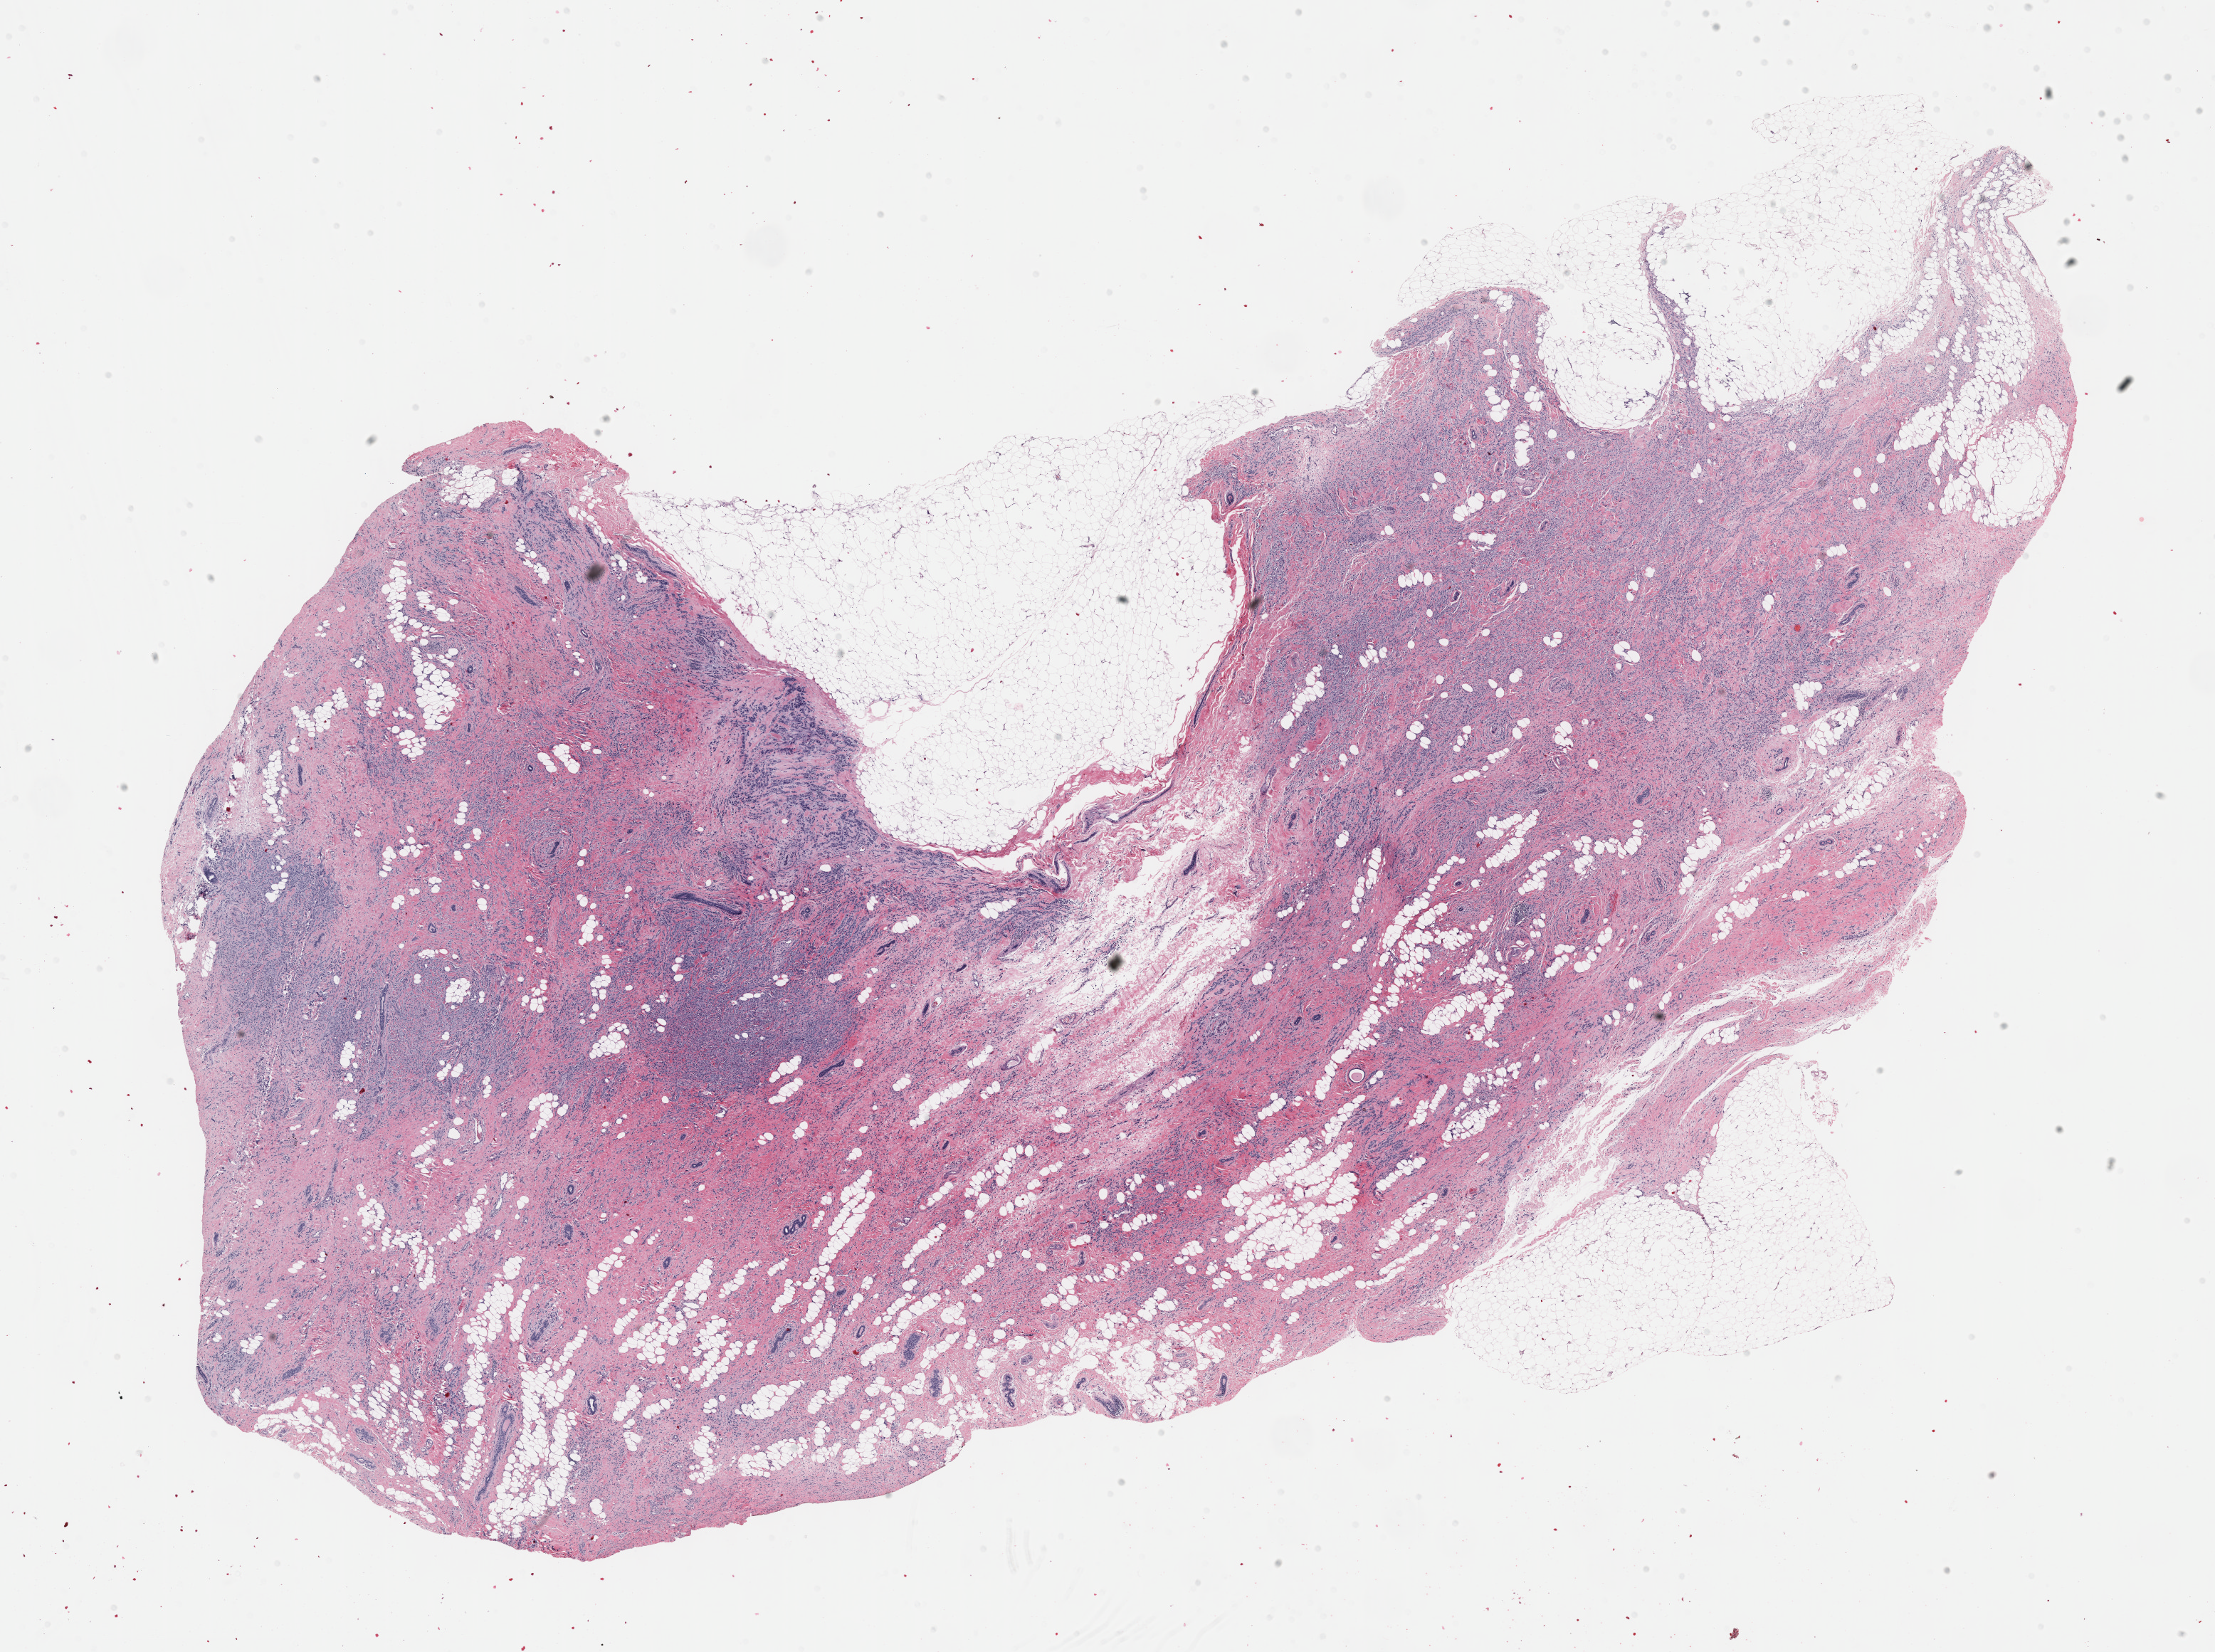
Whole-slide histology image, H&E-stained — whole scanned area (about 25.2 x 18.8 mm) shown as a low-resolution overview; FFPE section; sample: primary tumour, breast. Female patient; age at initial diagnosis 79 years.
• laterality: right
• AJCC pathologic stage: IIIC (7th edition)
• TNM: T3 N3a M0
• pathologic diagnosis: Infiltrating lobular mixed with other types of carcinoma
• lymph nodes positive (case pathology): 11 of 12 examined